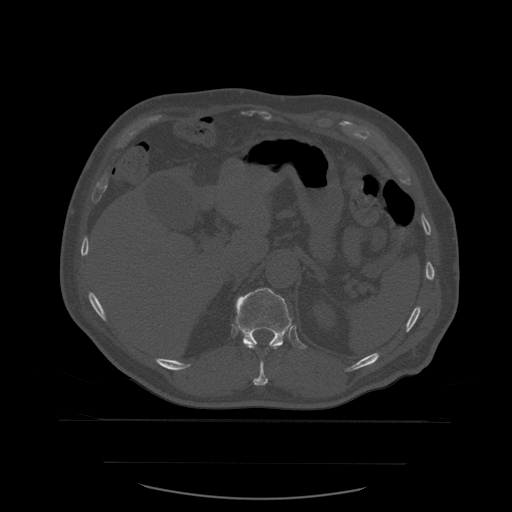
CT including the spine, one axial slice. Slice 281 of 590 in the series (ordered by position). Bone window (W 1800 / L 400 HU). 1.25 mm slice thickness. 512 × 512 image matrix, field of view 479 × 479 mm. Patient age 71 years. Case-level facts recorded for this patient, not image findings: primary cancer: lung; vertebrae with lytic lesions (as recorded): T1, T2, L5, S1.
Annotated regions visible in this slice (semi-automatic segmentation, software-assisted and operator-edited):
- T11 vertebra: bounding box (x1, y1, x2, y2) in pixels: (246, 346, 276, 386)
- T12 vertebra: (236, 288, 292, 349)